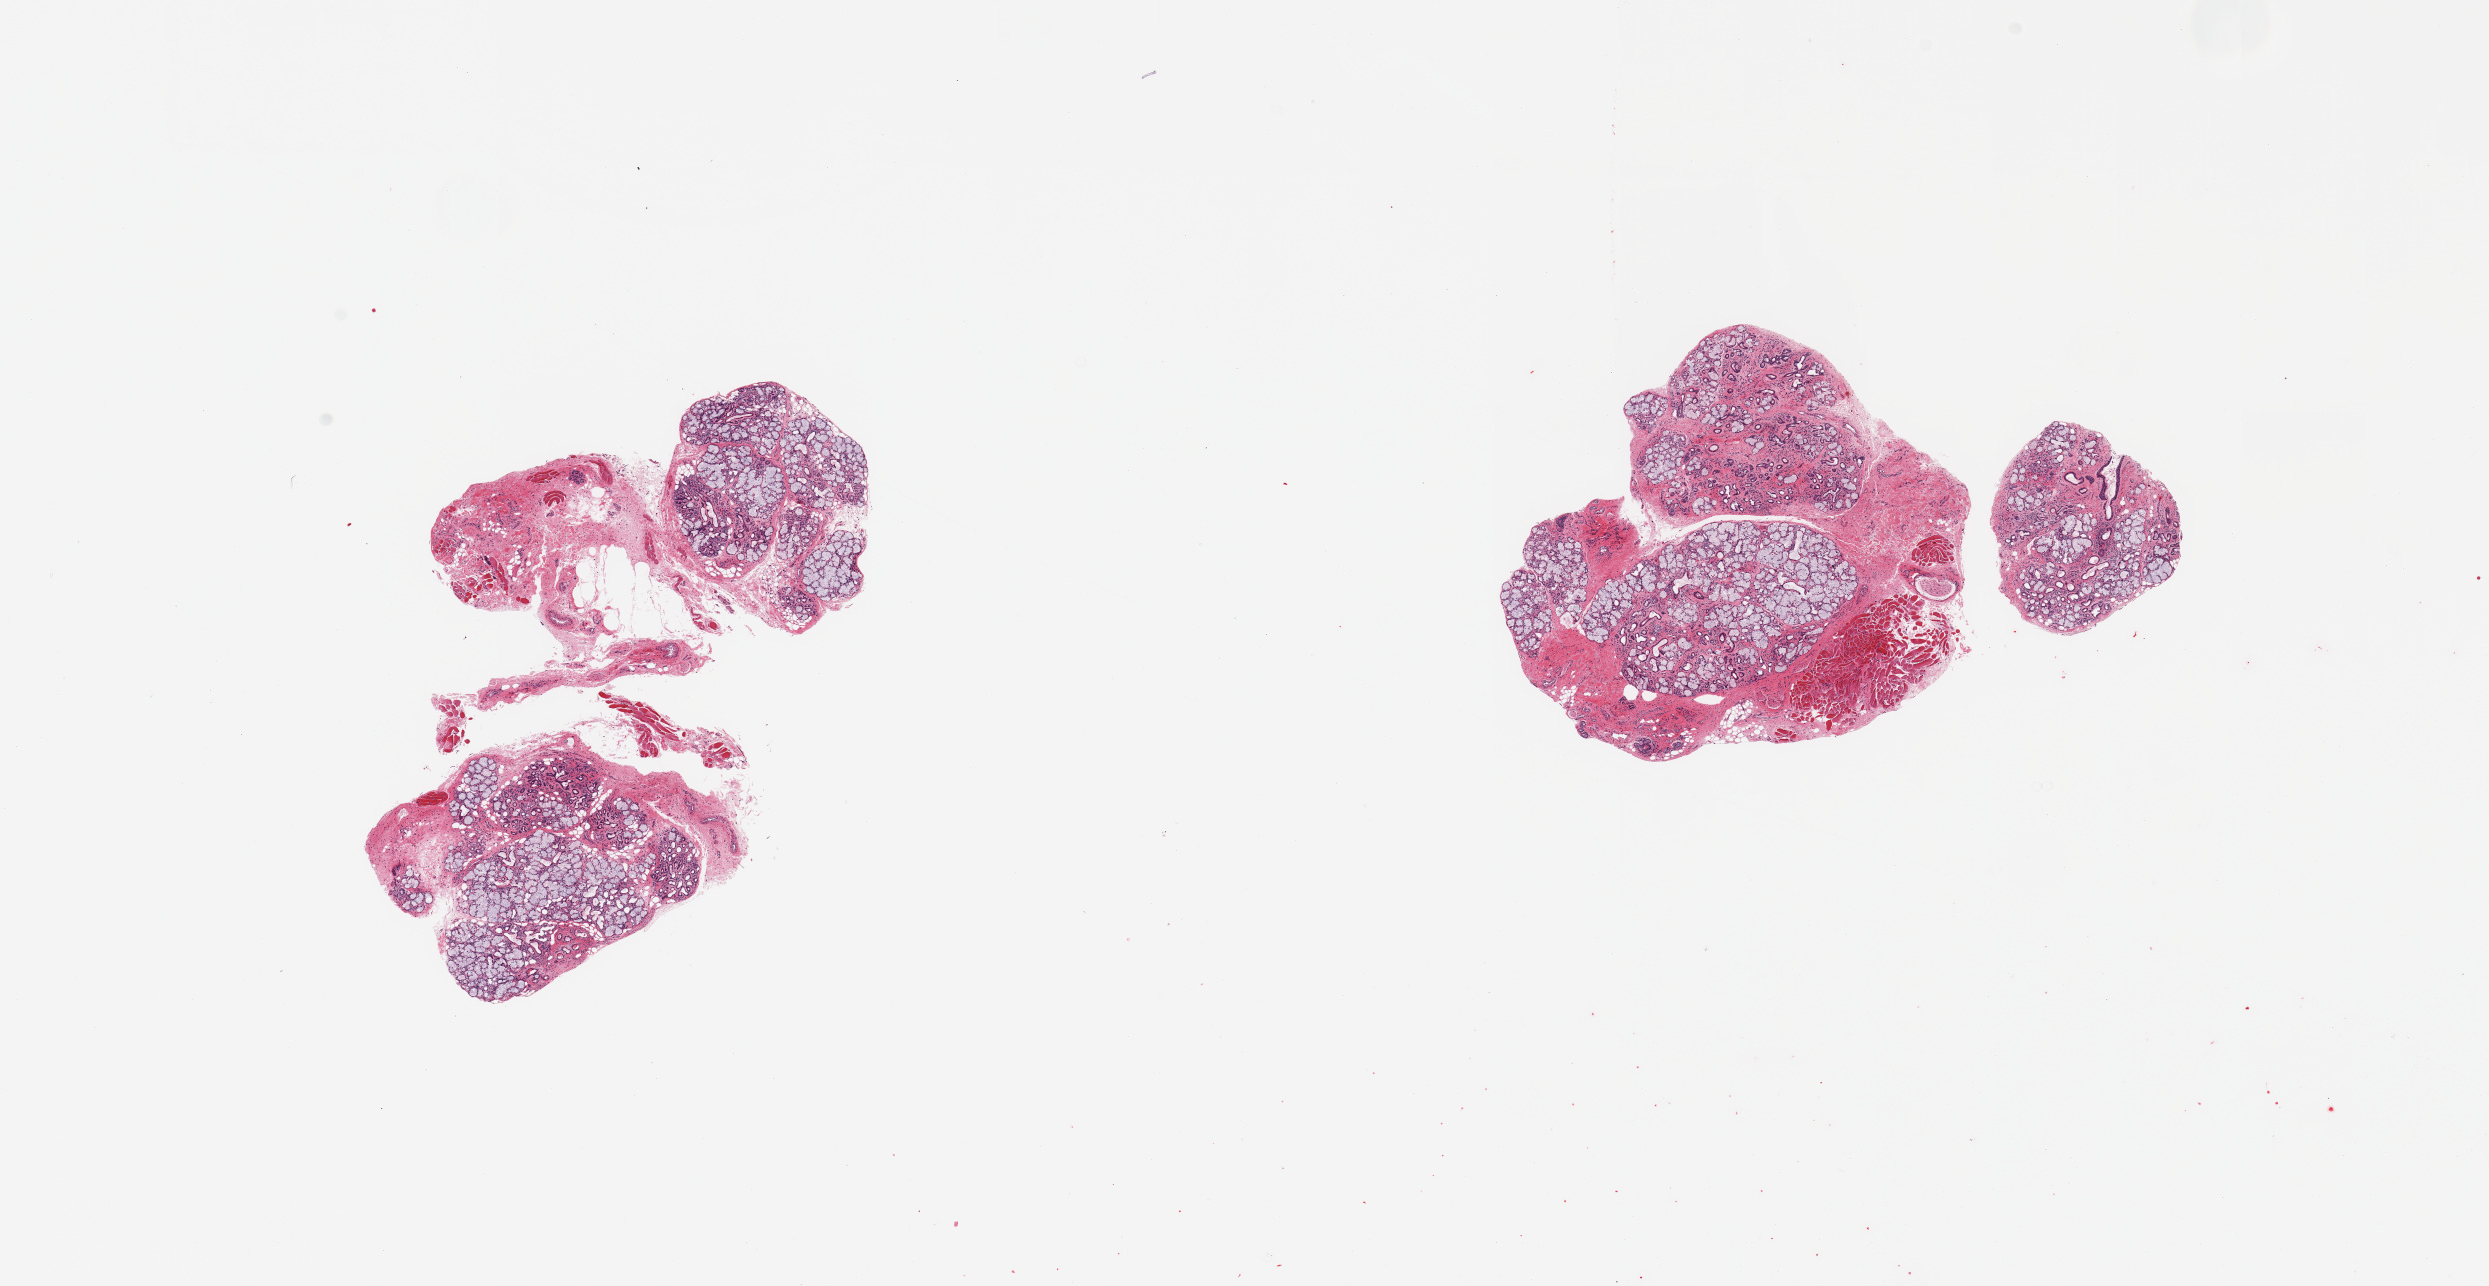
Whole-slide image, haematoxylin and eosin stain, shown as a low-resolution overview of the whole scanned area (about 19.7 x 10.2 mm); PAXgene-fixed paraffin-embedded (PFPE) section; section of minor salivary gland (target tissue); tissue donor sample. Donor sex: male.
Reviewer comment on this tissue sample: 4 pieces; focal atrophy & fibrosis; 30% fibromuscular stroma.